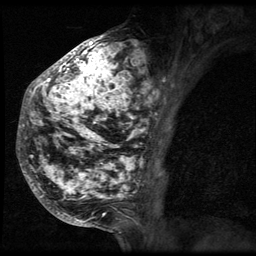
Breast MRI (dynamic contrast-enhanced), one sagittal slice; position 26 of 64 along the scan axis; 3 images stored at this slice position (order not interpretable as contrast timing); 1.5 T; TE 4.2 ms, TR 9 ms; 2.5 mm slice thickness; 256 × 256 image matrix. Patient: female, 50 years. From the clinical record (not read from this slice): setting: breast cancer imaged before/during neoadjuvant chemotherapy; receptor status: triple-negative.
Outlined on this slice (semi-automatic segmentation, software-assisted and operator-edited):
- analysis volume of interest (the breast-tissue region the enhancement analysis was run in; not a lesion): bounding box <24,39,158,212> (left, top, right, bottom; pixels)
- tumour enhancement mask (voxels above the 140 % enhancement threshold inside the analysis volume of interest): <24,39,158,201>